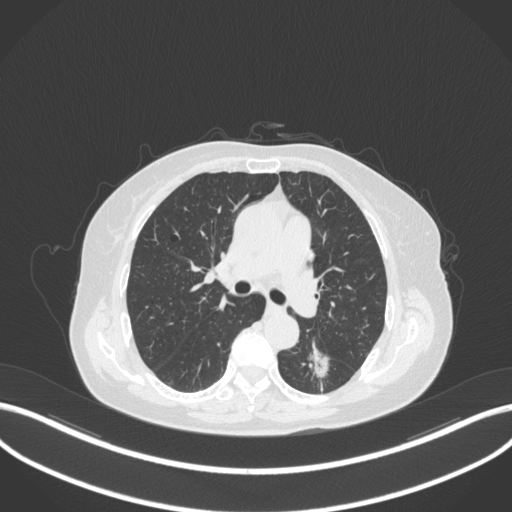
Chest CT, one axial slice. Position 180 of 352 along the scan axis. Lung window (W 1500 / L -600 HU). 512 × 512 image matrix, field of view 400 × 400 mm. Patient: female, 70 years. Case-level facts recorded for this patient, not image findings: clinical TNM (as recorded): T1c N0 M0.
Structures marked on this image (rectangle marked by the reading radiologist):
- lung tumour (recorded histology: adenocarcinoma): bounding box (x1, y1, x2, y2) in pixels: (300, 337, 331, 381)